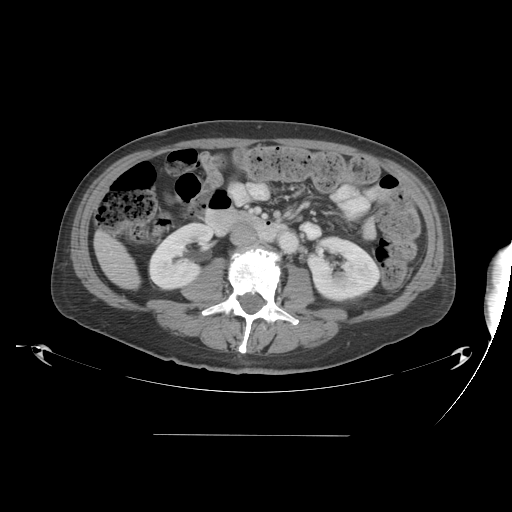
Contrast-enhanced abdominal CT, one axial slice. Slice 11 of 48 in the series (ordered by position). Reconstruction kernel STANDARD. 120 kVp. Intravenous contrast given. Soft-tissue window (W 400 / L 40 HU). 5 mm slice thickness. 512 × 512 image matrix, field of view 486 × 486 mm. Male patient, age 65 years. Case-level facts recorded for this patient, not image findings: diagnosis: colorectal cancer liver metastases, imaged before liver resection; multiple liver metastases: yes; largest metastasis: 11 cm.
Structures marked on this image (manually delineated by an expert):
- liver: bounding box (x1, y1, x2, y2) in pixels: (96, 234, 138, 287)